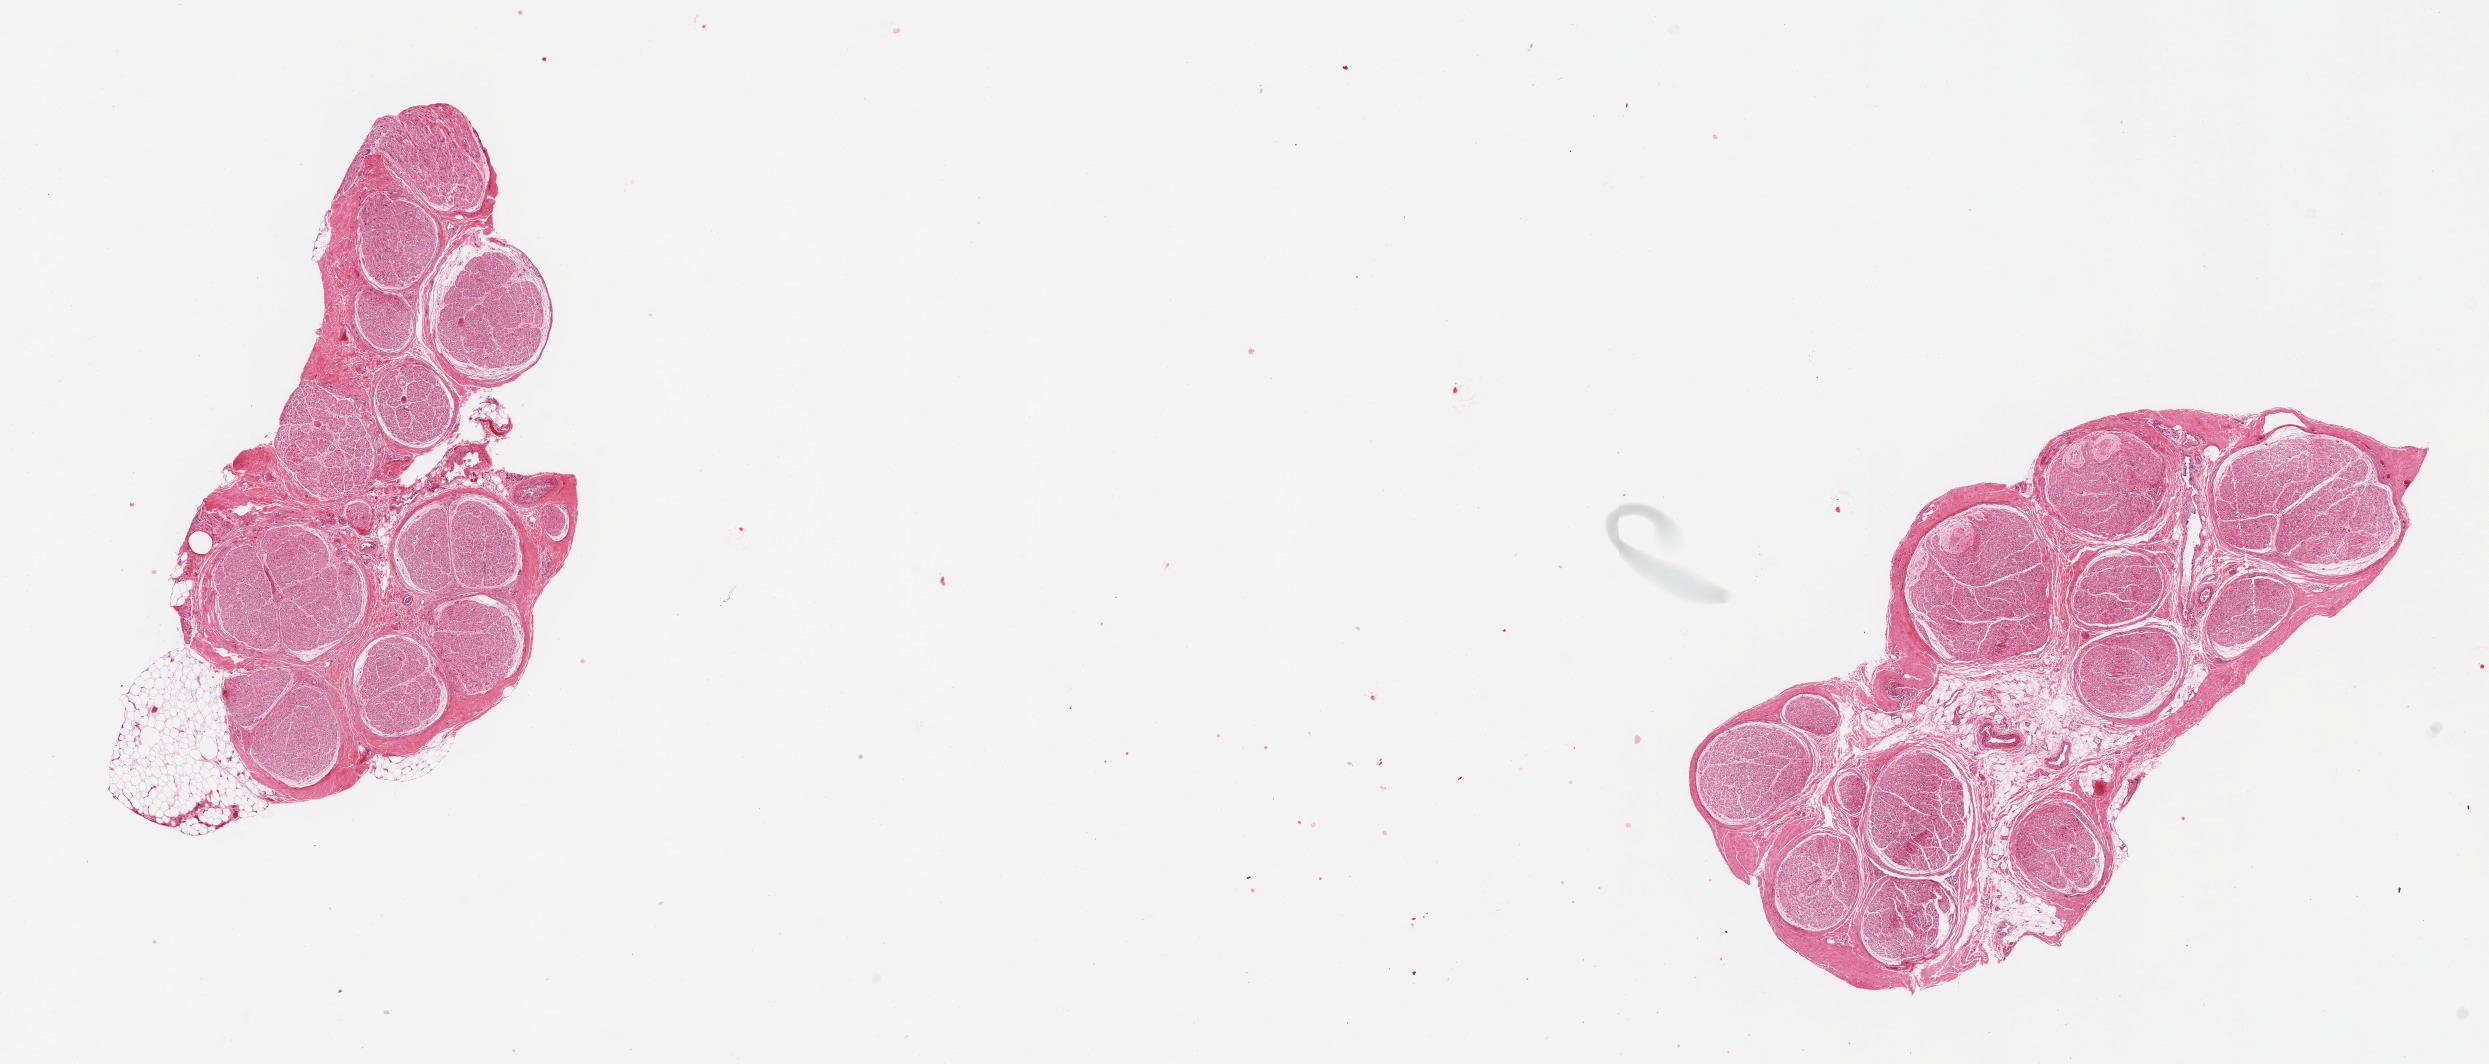
Whole-slide image, H&E stain, a low-resolution overview of the entire scanned area, about 19.7 x 8.4 mm, PAXgene-fixed paraffin-embedded (PFPE) section, target tissue: tibial nerve, tissue donor sample.
Reviewer comment on this tissue sample: 2 pieces, ~1mm nubbin of adherent fat.